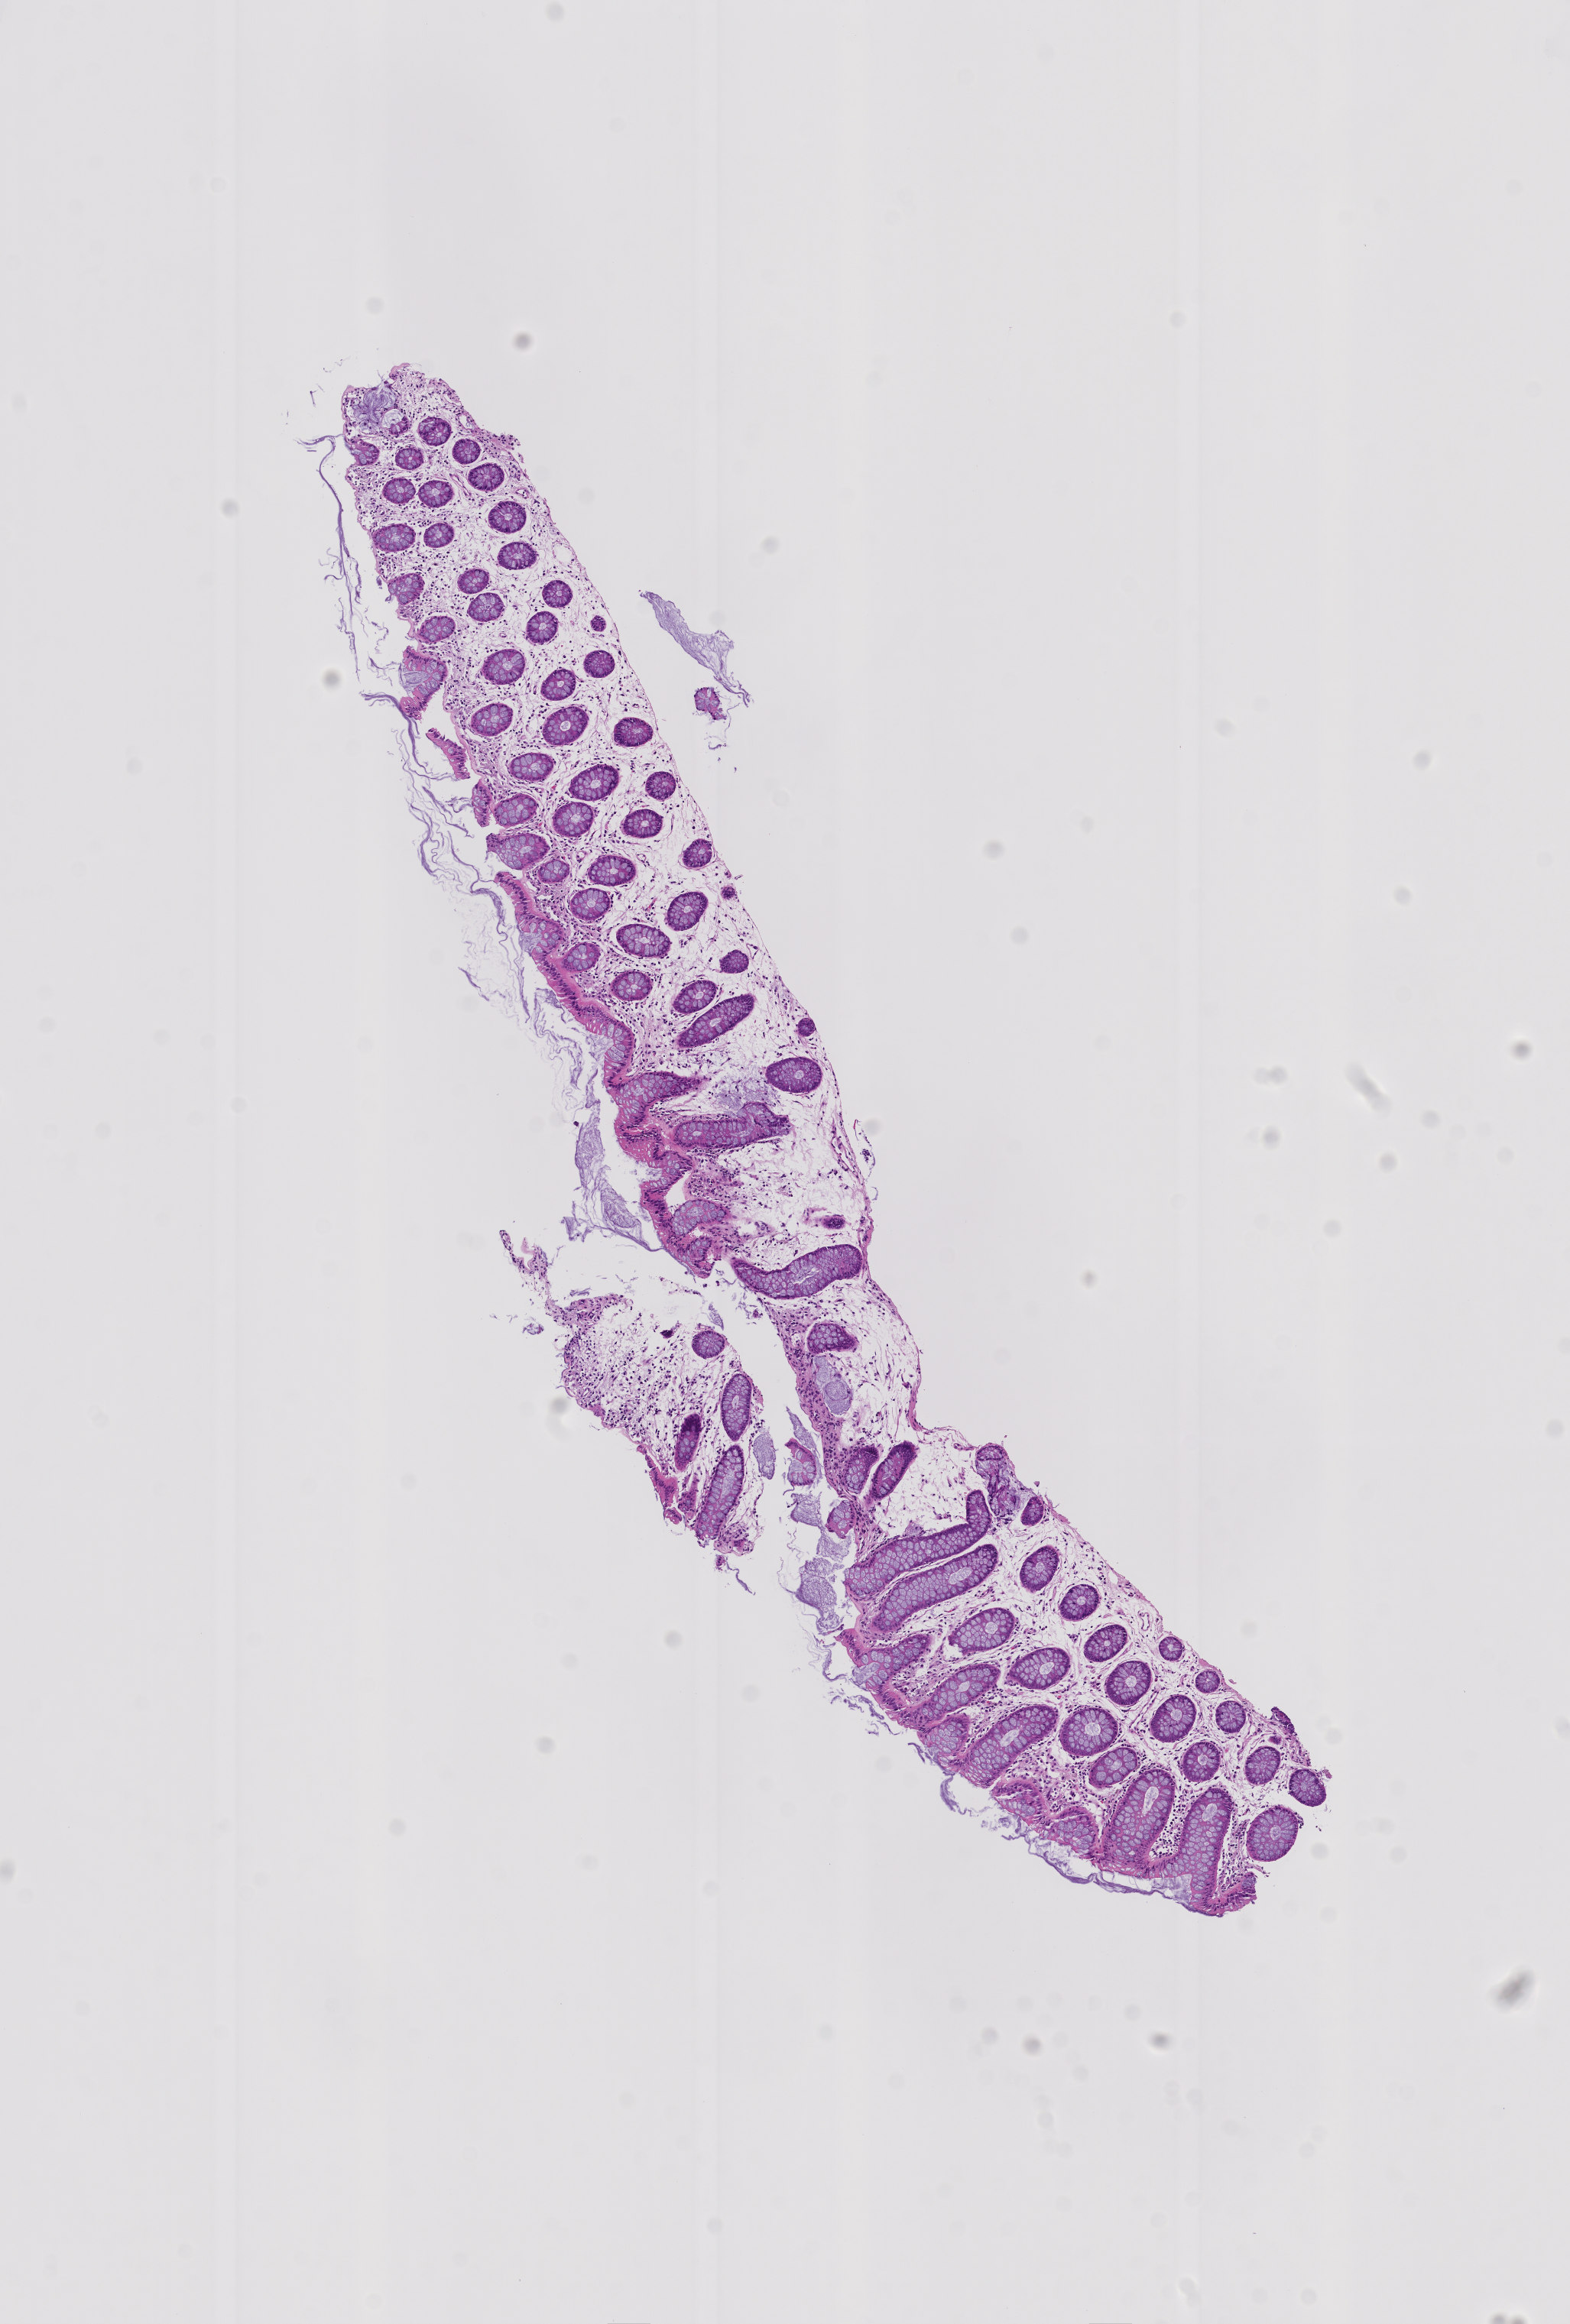
Whole-slide image, hematoxylin and eosin (H&E) stain: colon biopsy — low-resolution overview of the scanned area, about 4.1 x 6.1 mm. FFPE section. Site: sigmoid colon. Patient sex: male.
Lesion category (as recorded): hyperplasia.